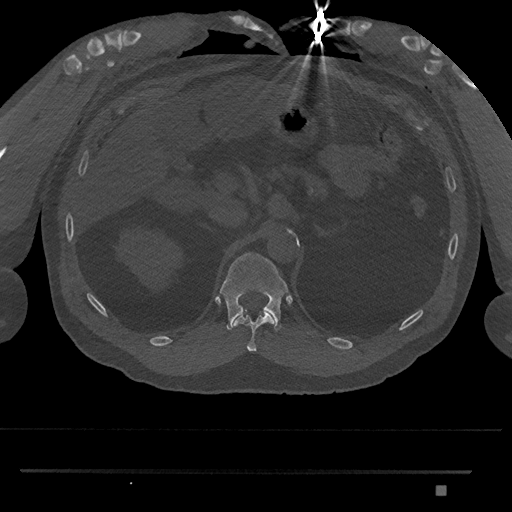
CT including the spine, one axial slice. Slice 911 of 1134 in the series (ordered by position). Reconstruction kernel Br40s/3. 120 kVp. Bone window (W 1800 / L 400 HU). 512 × 512 image matrix. Male patient, age 65 years. From the clinical record (not read from this slice): primary cancer: prostate.
Outlined on this slice (semi-automatic segmentation, software-assisted and operator-edited):
- T11 vertebra: bounding box (x1, y1, x2, y2) in pixels: (234, 311, 274, 352)
- T12 vertebra: (220, 252, 289, 331)